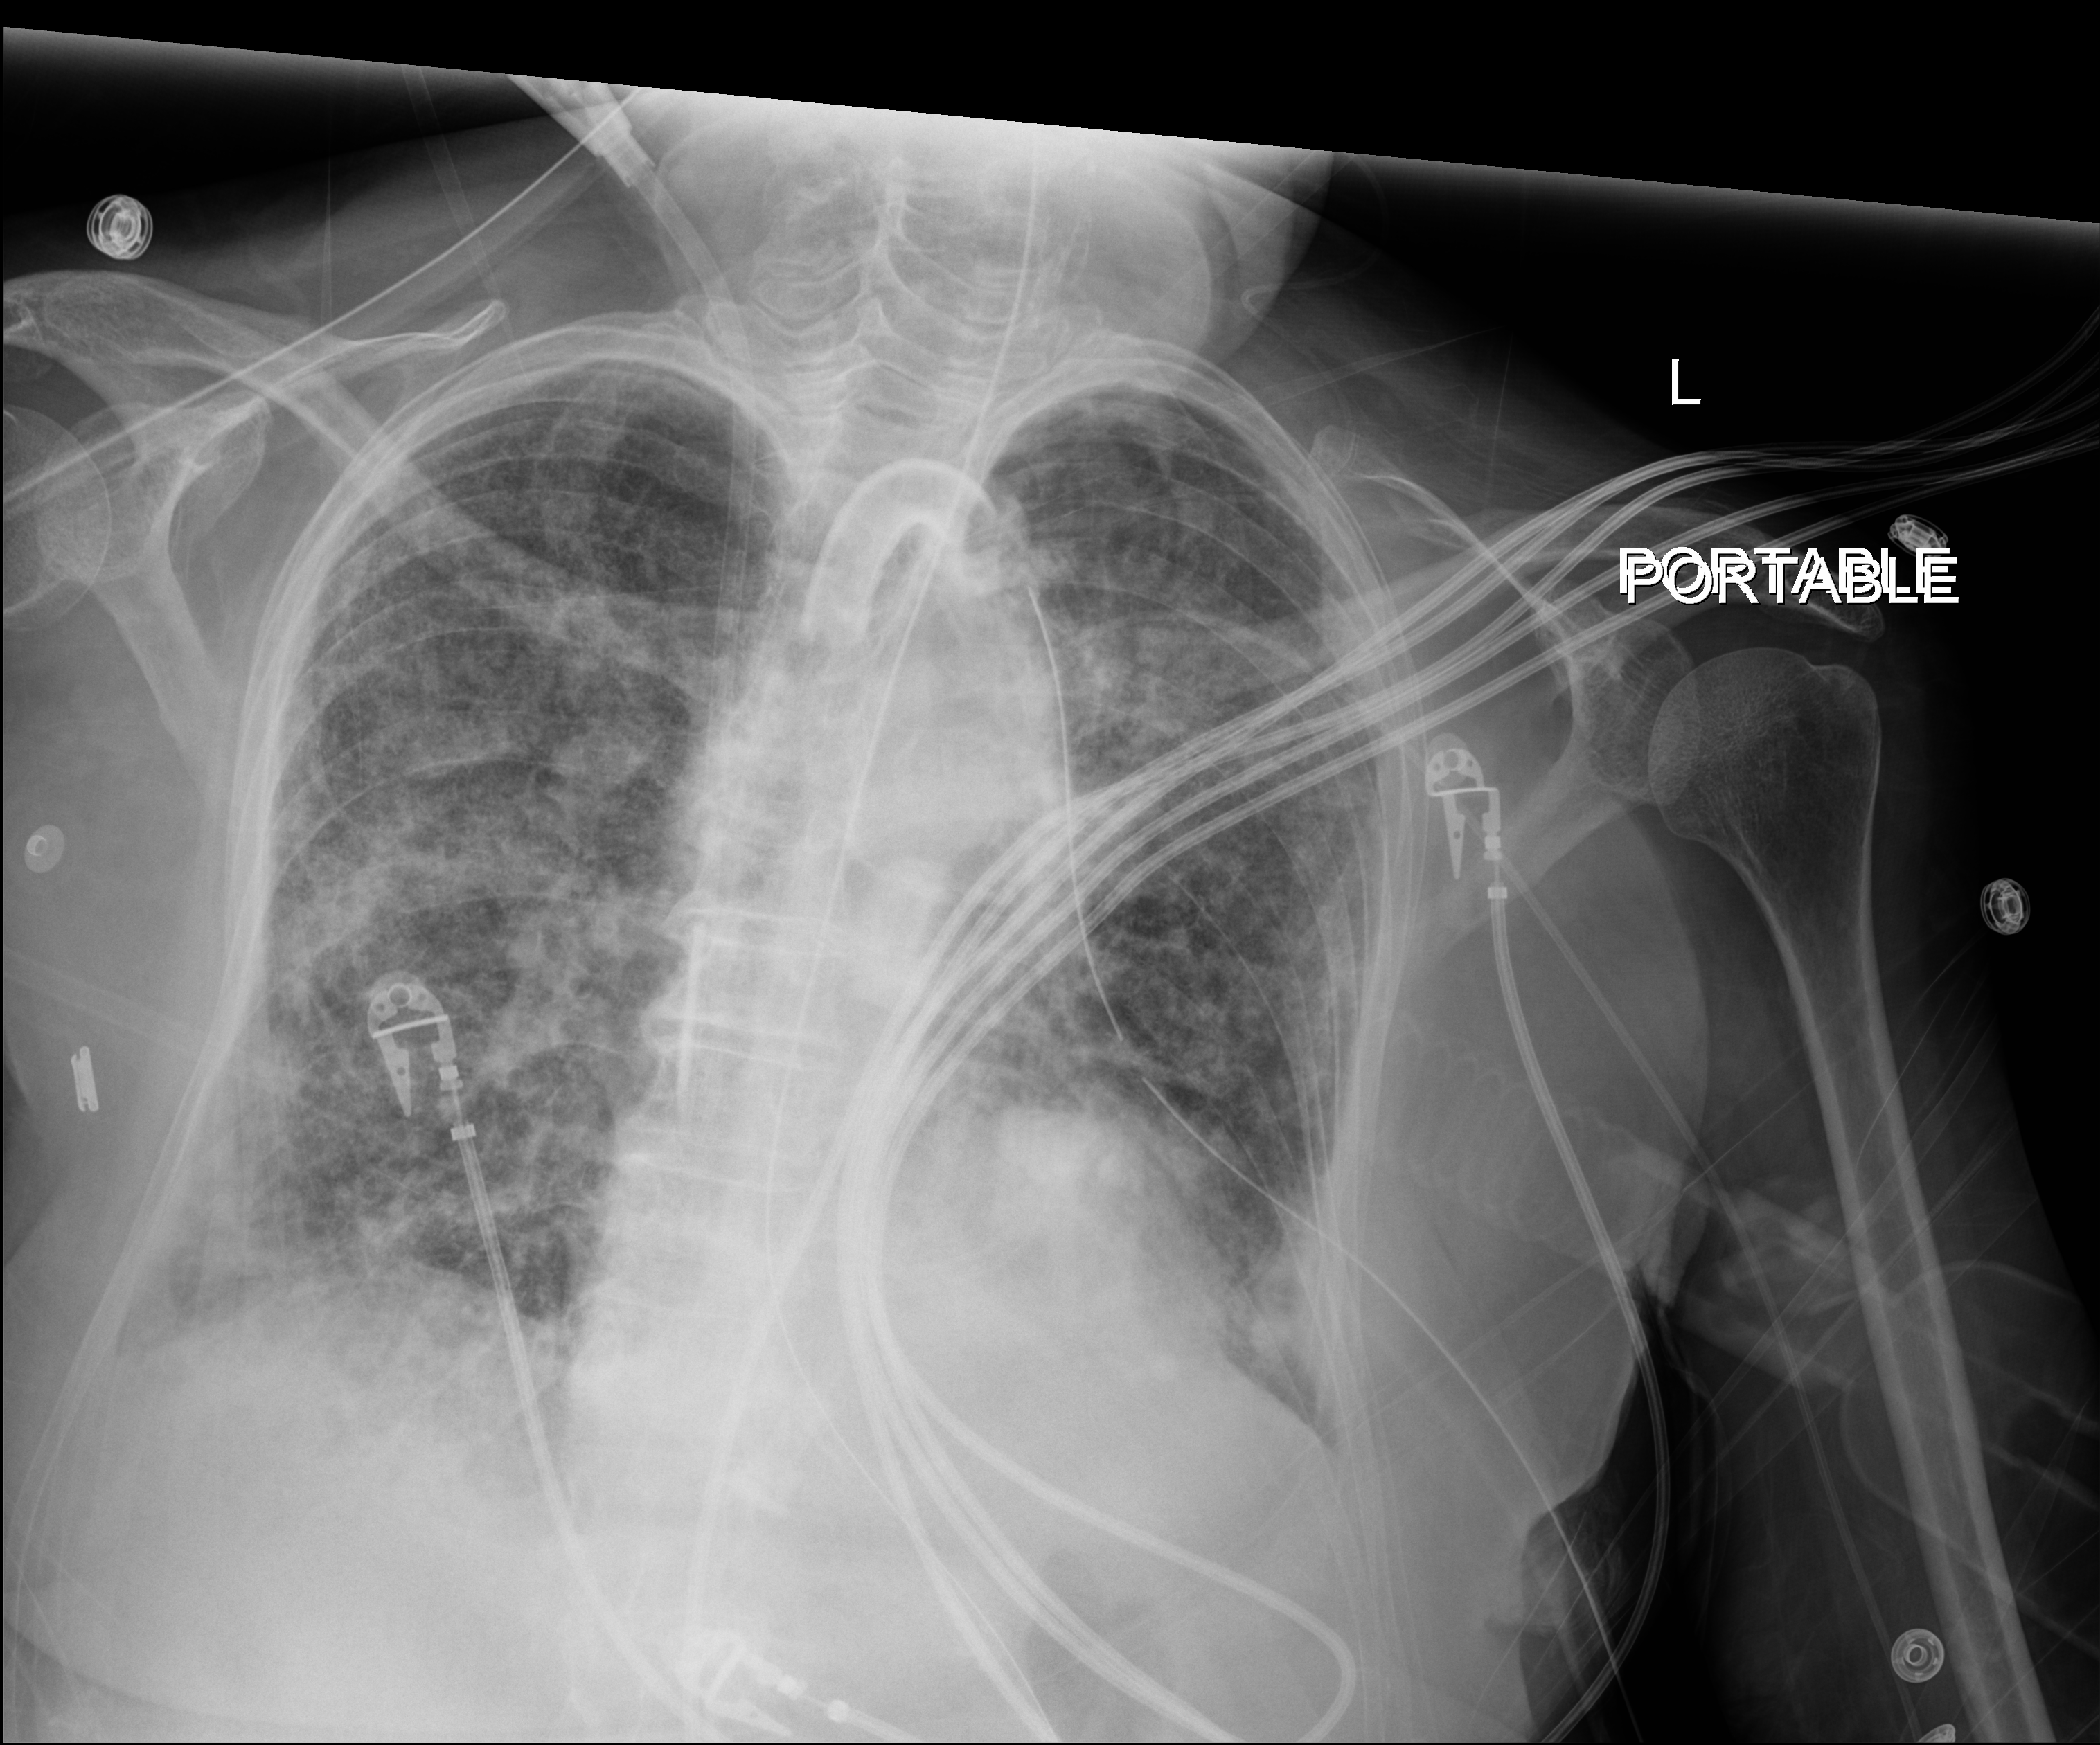
Chest X-ray (portable). Female patient hospitalised with COVID-19, age 75–90 years.
Admission-level facts for this patient (not findings on this image; timing relative to this image not recorded): admitted to intensive care during this hospital stay: yes; mechanically ventilated during this hospital stay: yes; length of hospital stay: 70 days.